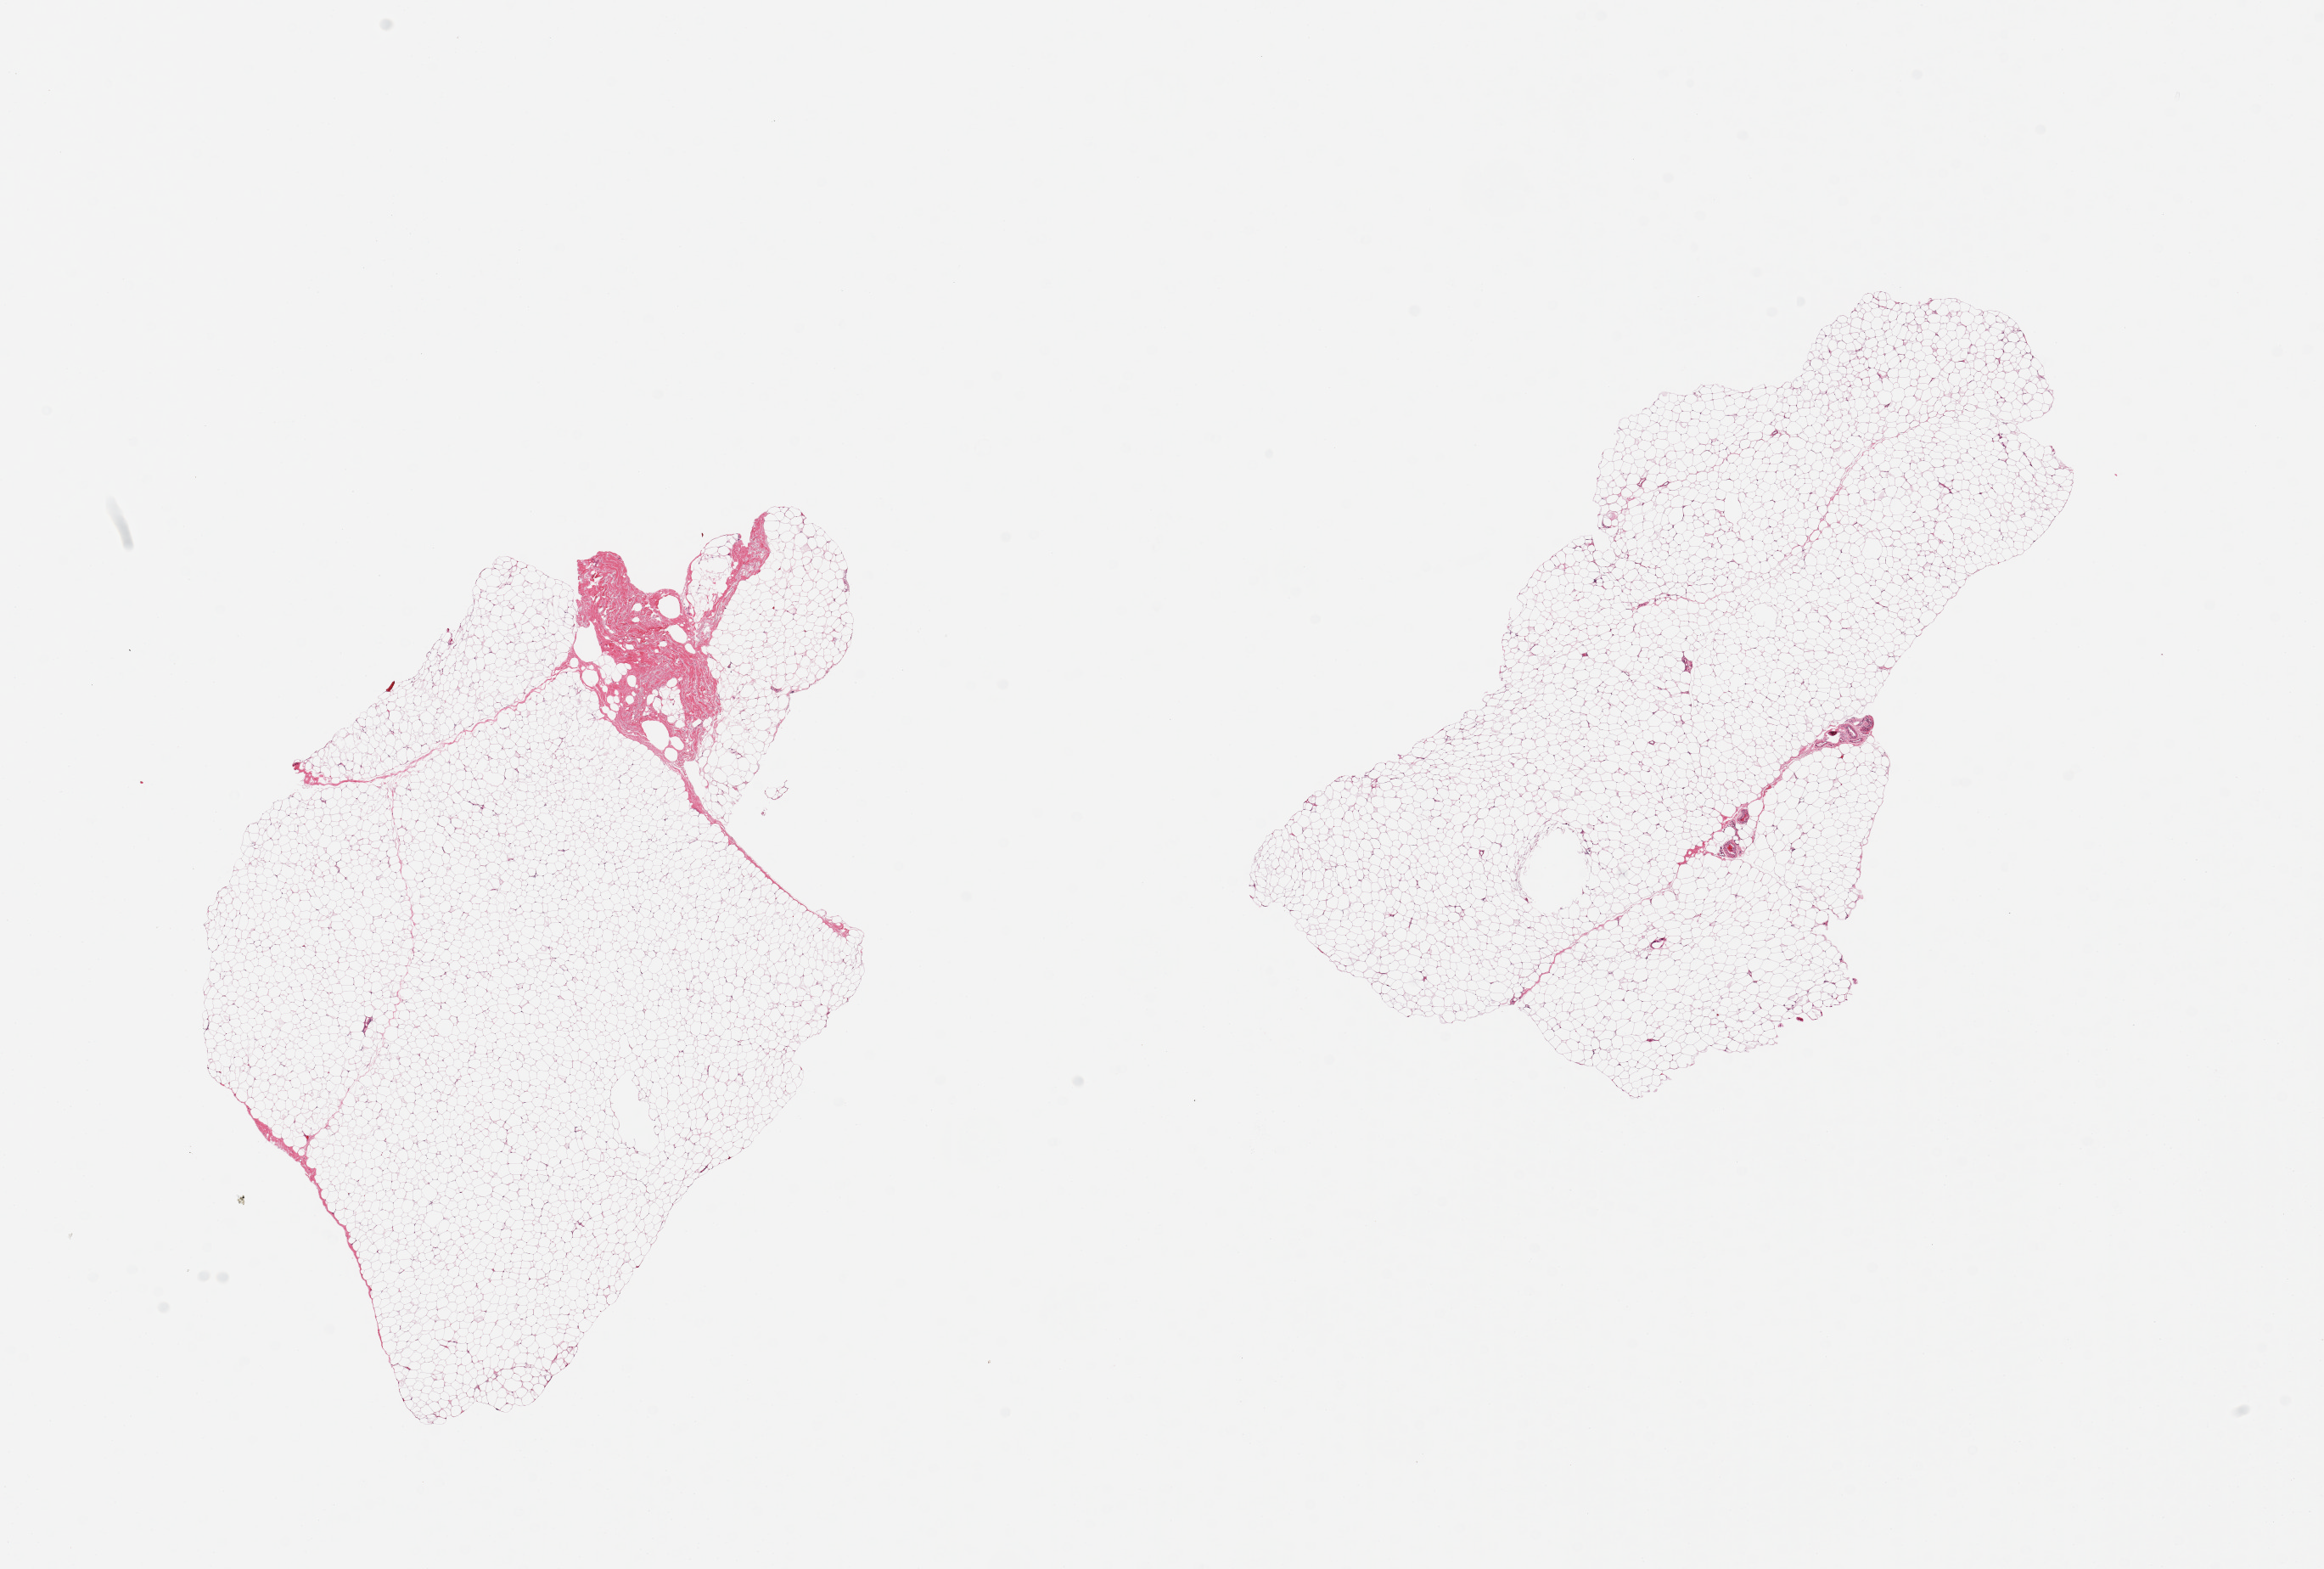
Digitized H&E-stained section, brightfield, shown as a low-resolution overview of the whole scanned area (about 21.7 x 14.6 mm, slide scanned at 20x); PAXgene-fixed, paraffin-embedded tissue; section of breast (target tissue); donor tissue sample.
Reviewer comment on this tissue sample: 2 pieces; fat with small focus of fibrous tissue, not ductal elements seen.